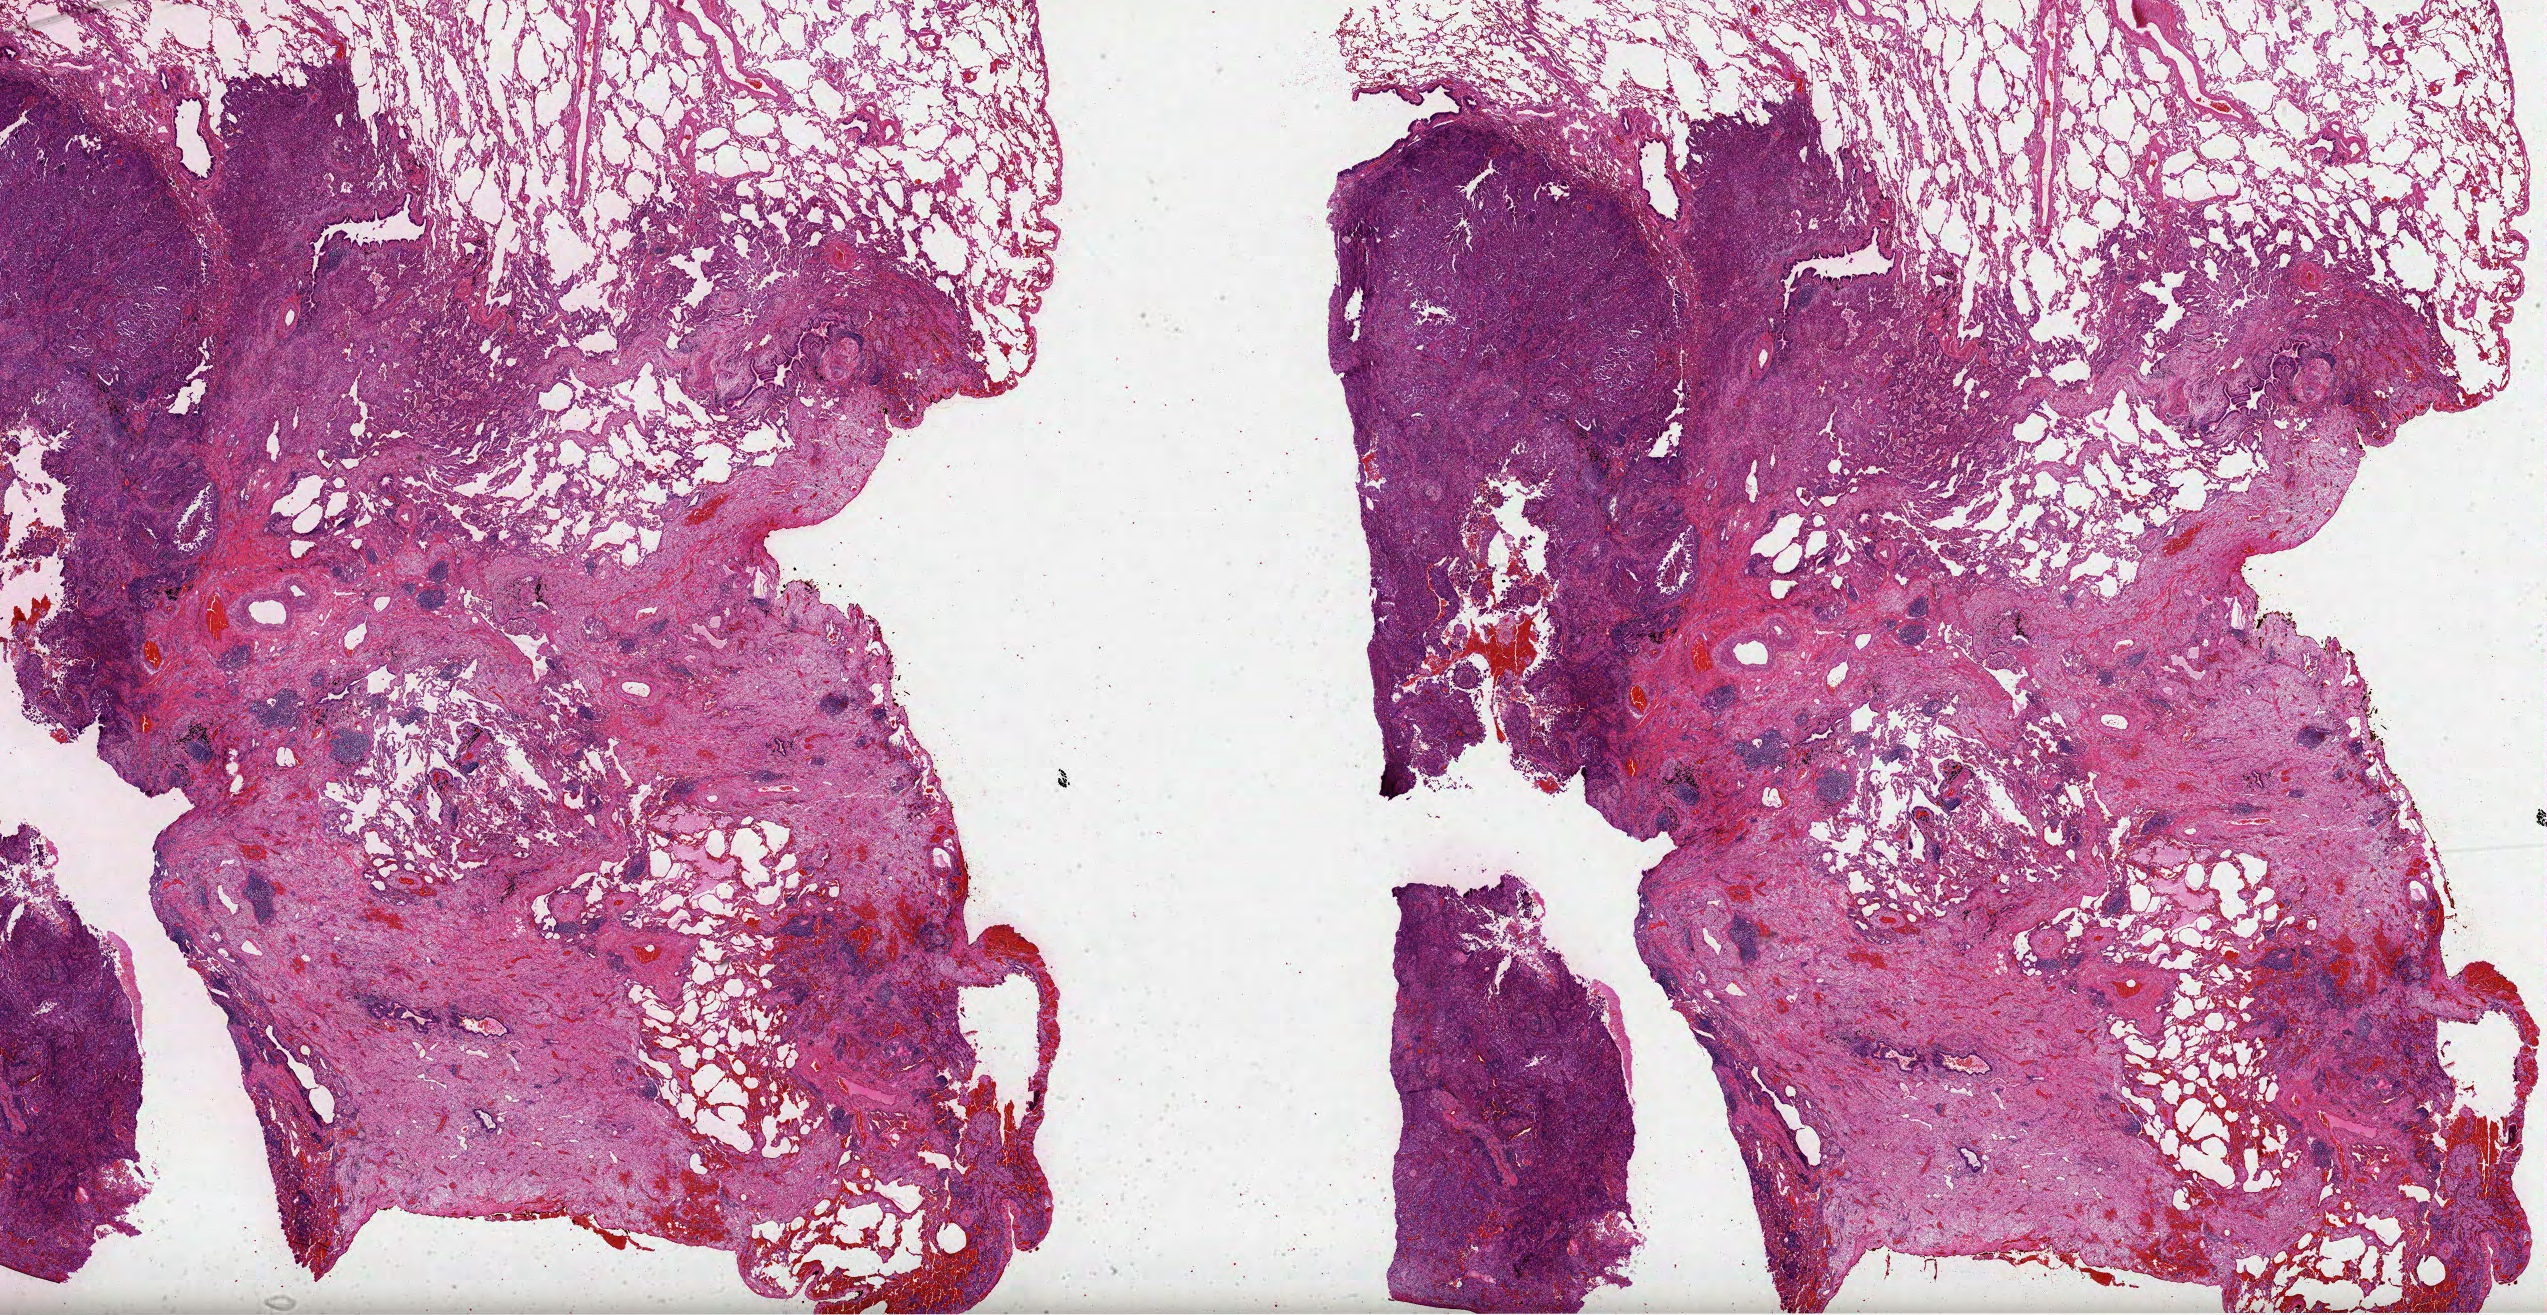
Digitized H&E-stained tissue section (whole slide), low-resolution overview of the scanned area, about 41.1 x 21.2 mm; formalin-fixed paraffin-embedded (FFPE) diagnostic section; primary tumour sample from the lung. Patient: male, age at initial diagnosis 82 years.
- AJCC pathologic stage: IIIA (7th edition)
- diagnosis: Papillary adenocarcinoma, NOS
- laterality: left